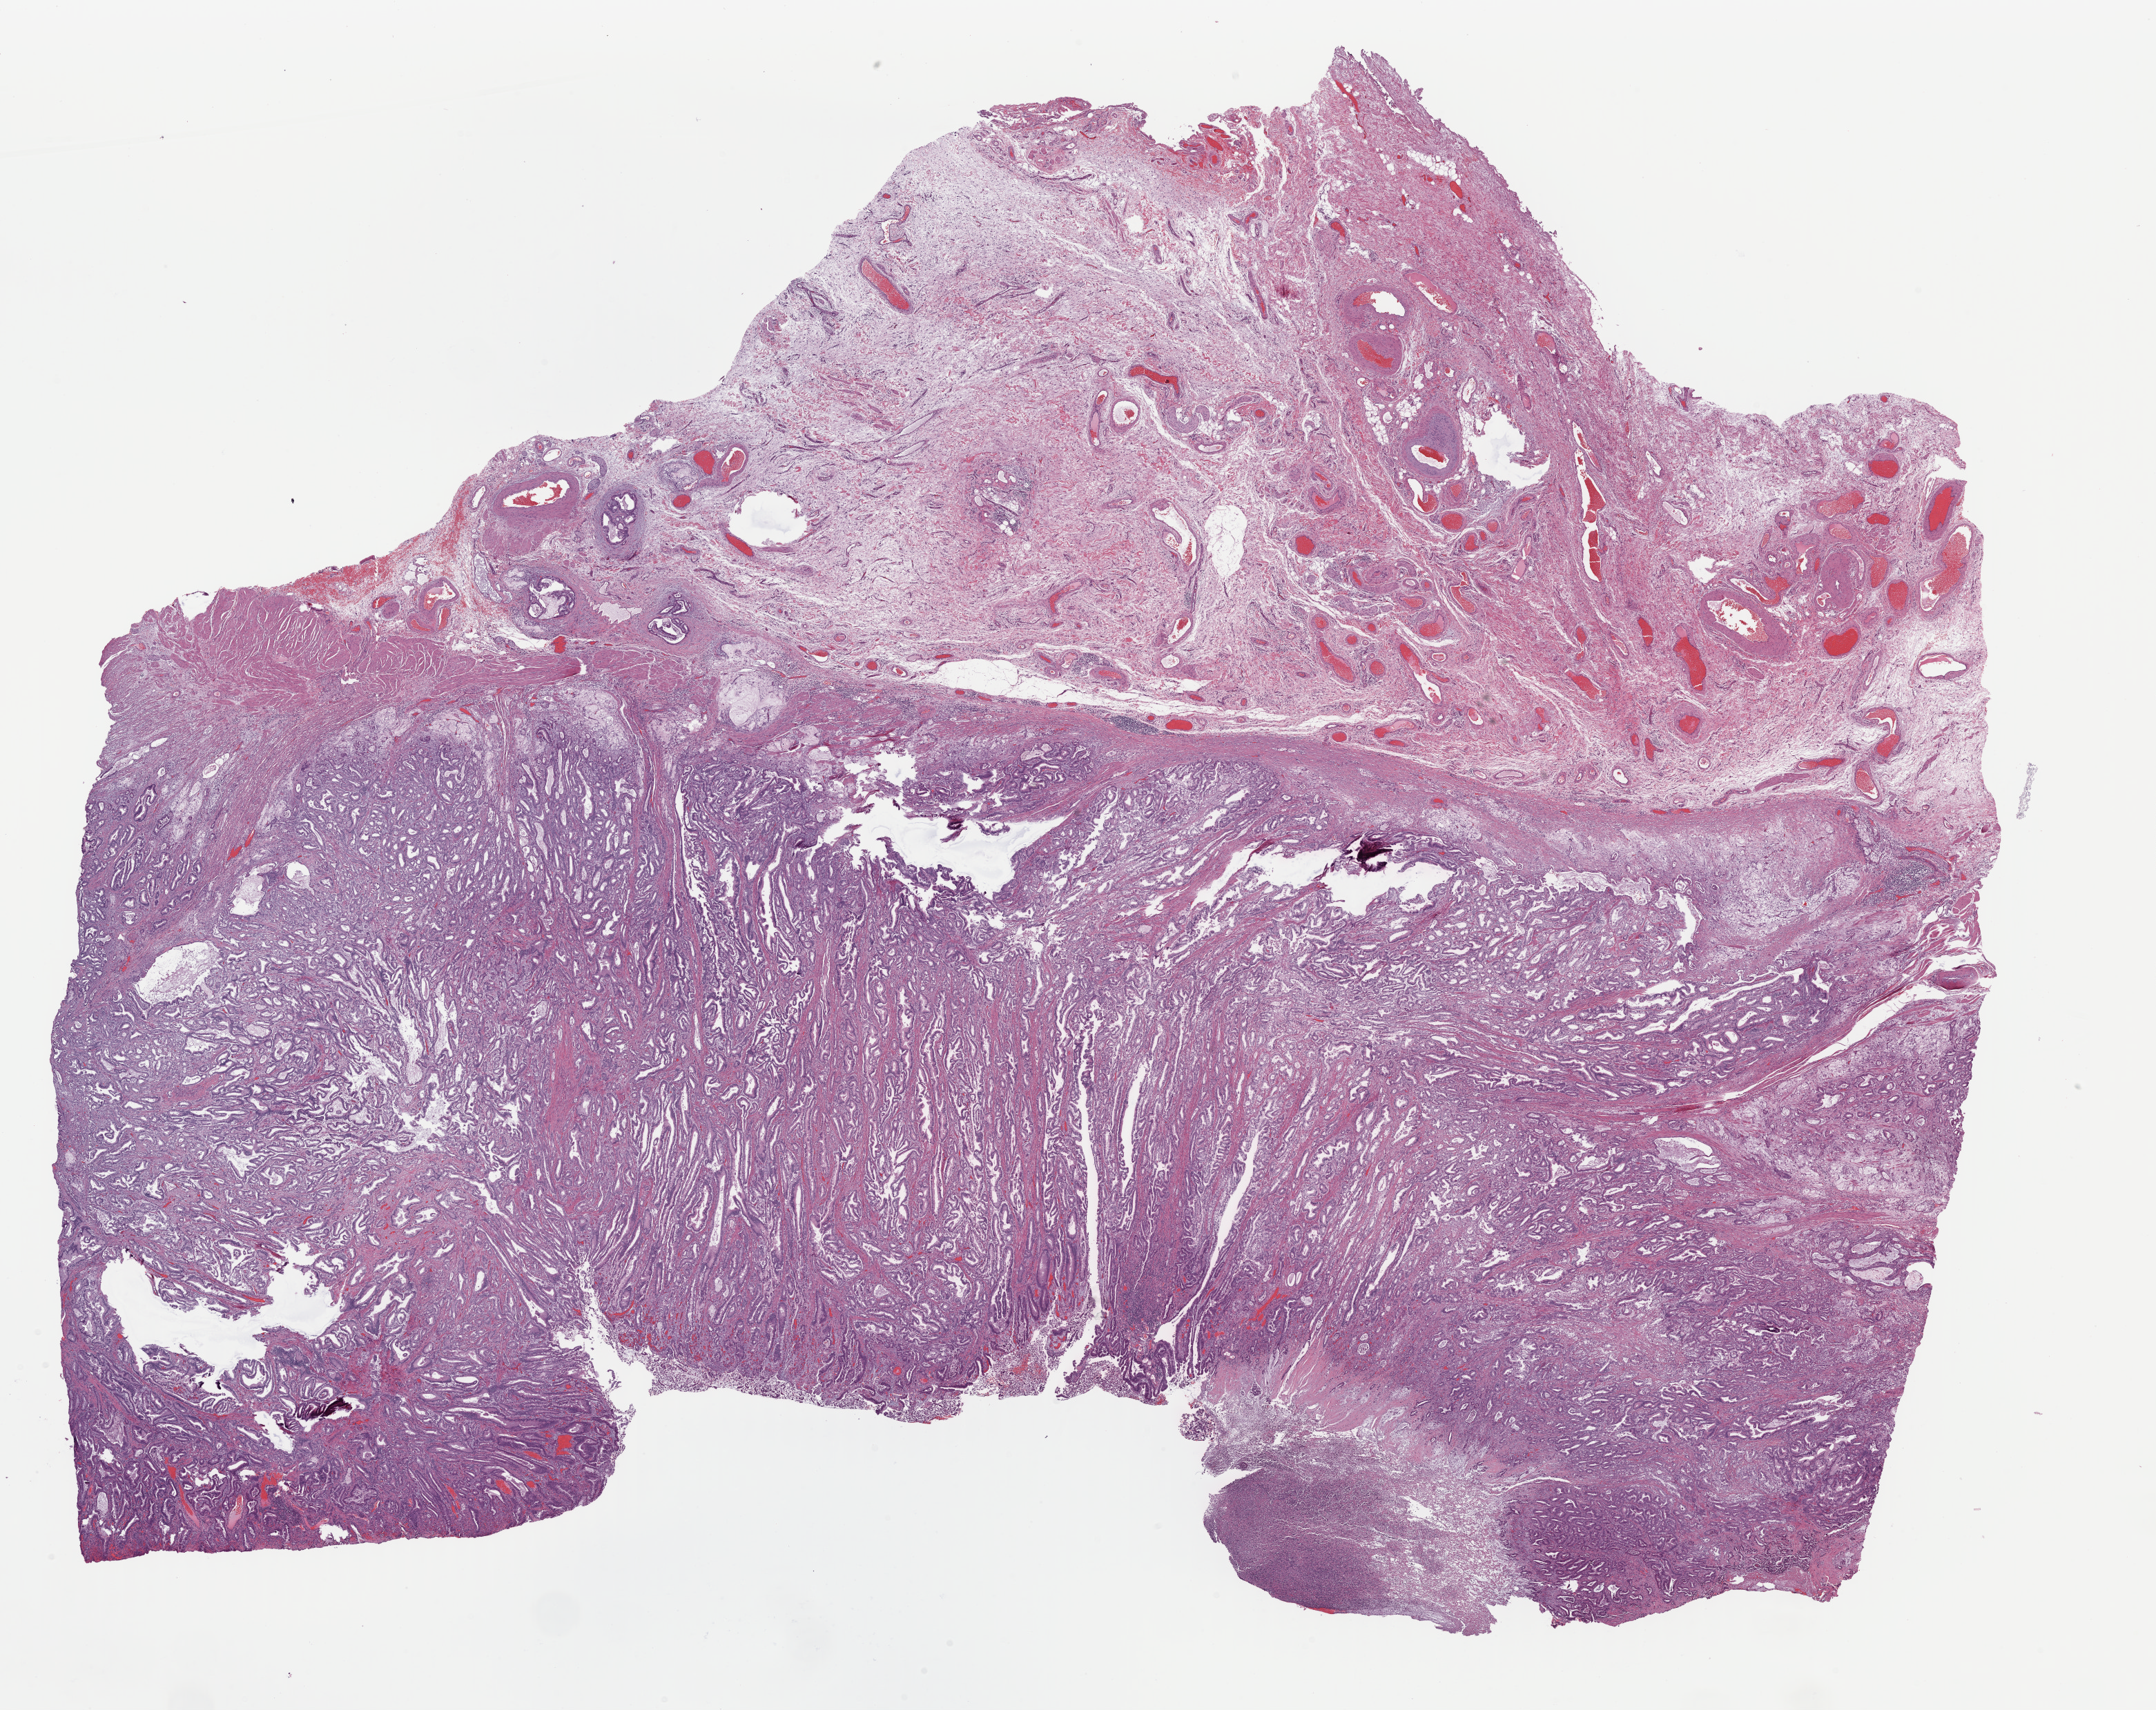
Whole-slide histology image, H&E-stained, shown as a low-resolution overview of the whole scanned area (about 24.6 x 19.5 mm); formalin-fixed paraffin-embedded (FFPE) diagnostic section; primary tumour sample from the esophagus. Female, age 84 years at initial diagnosis.
Diagnosis: Adenocarcinoma, NOS (lower third of esophagus).